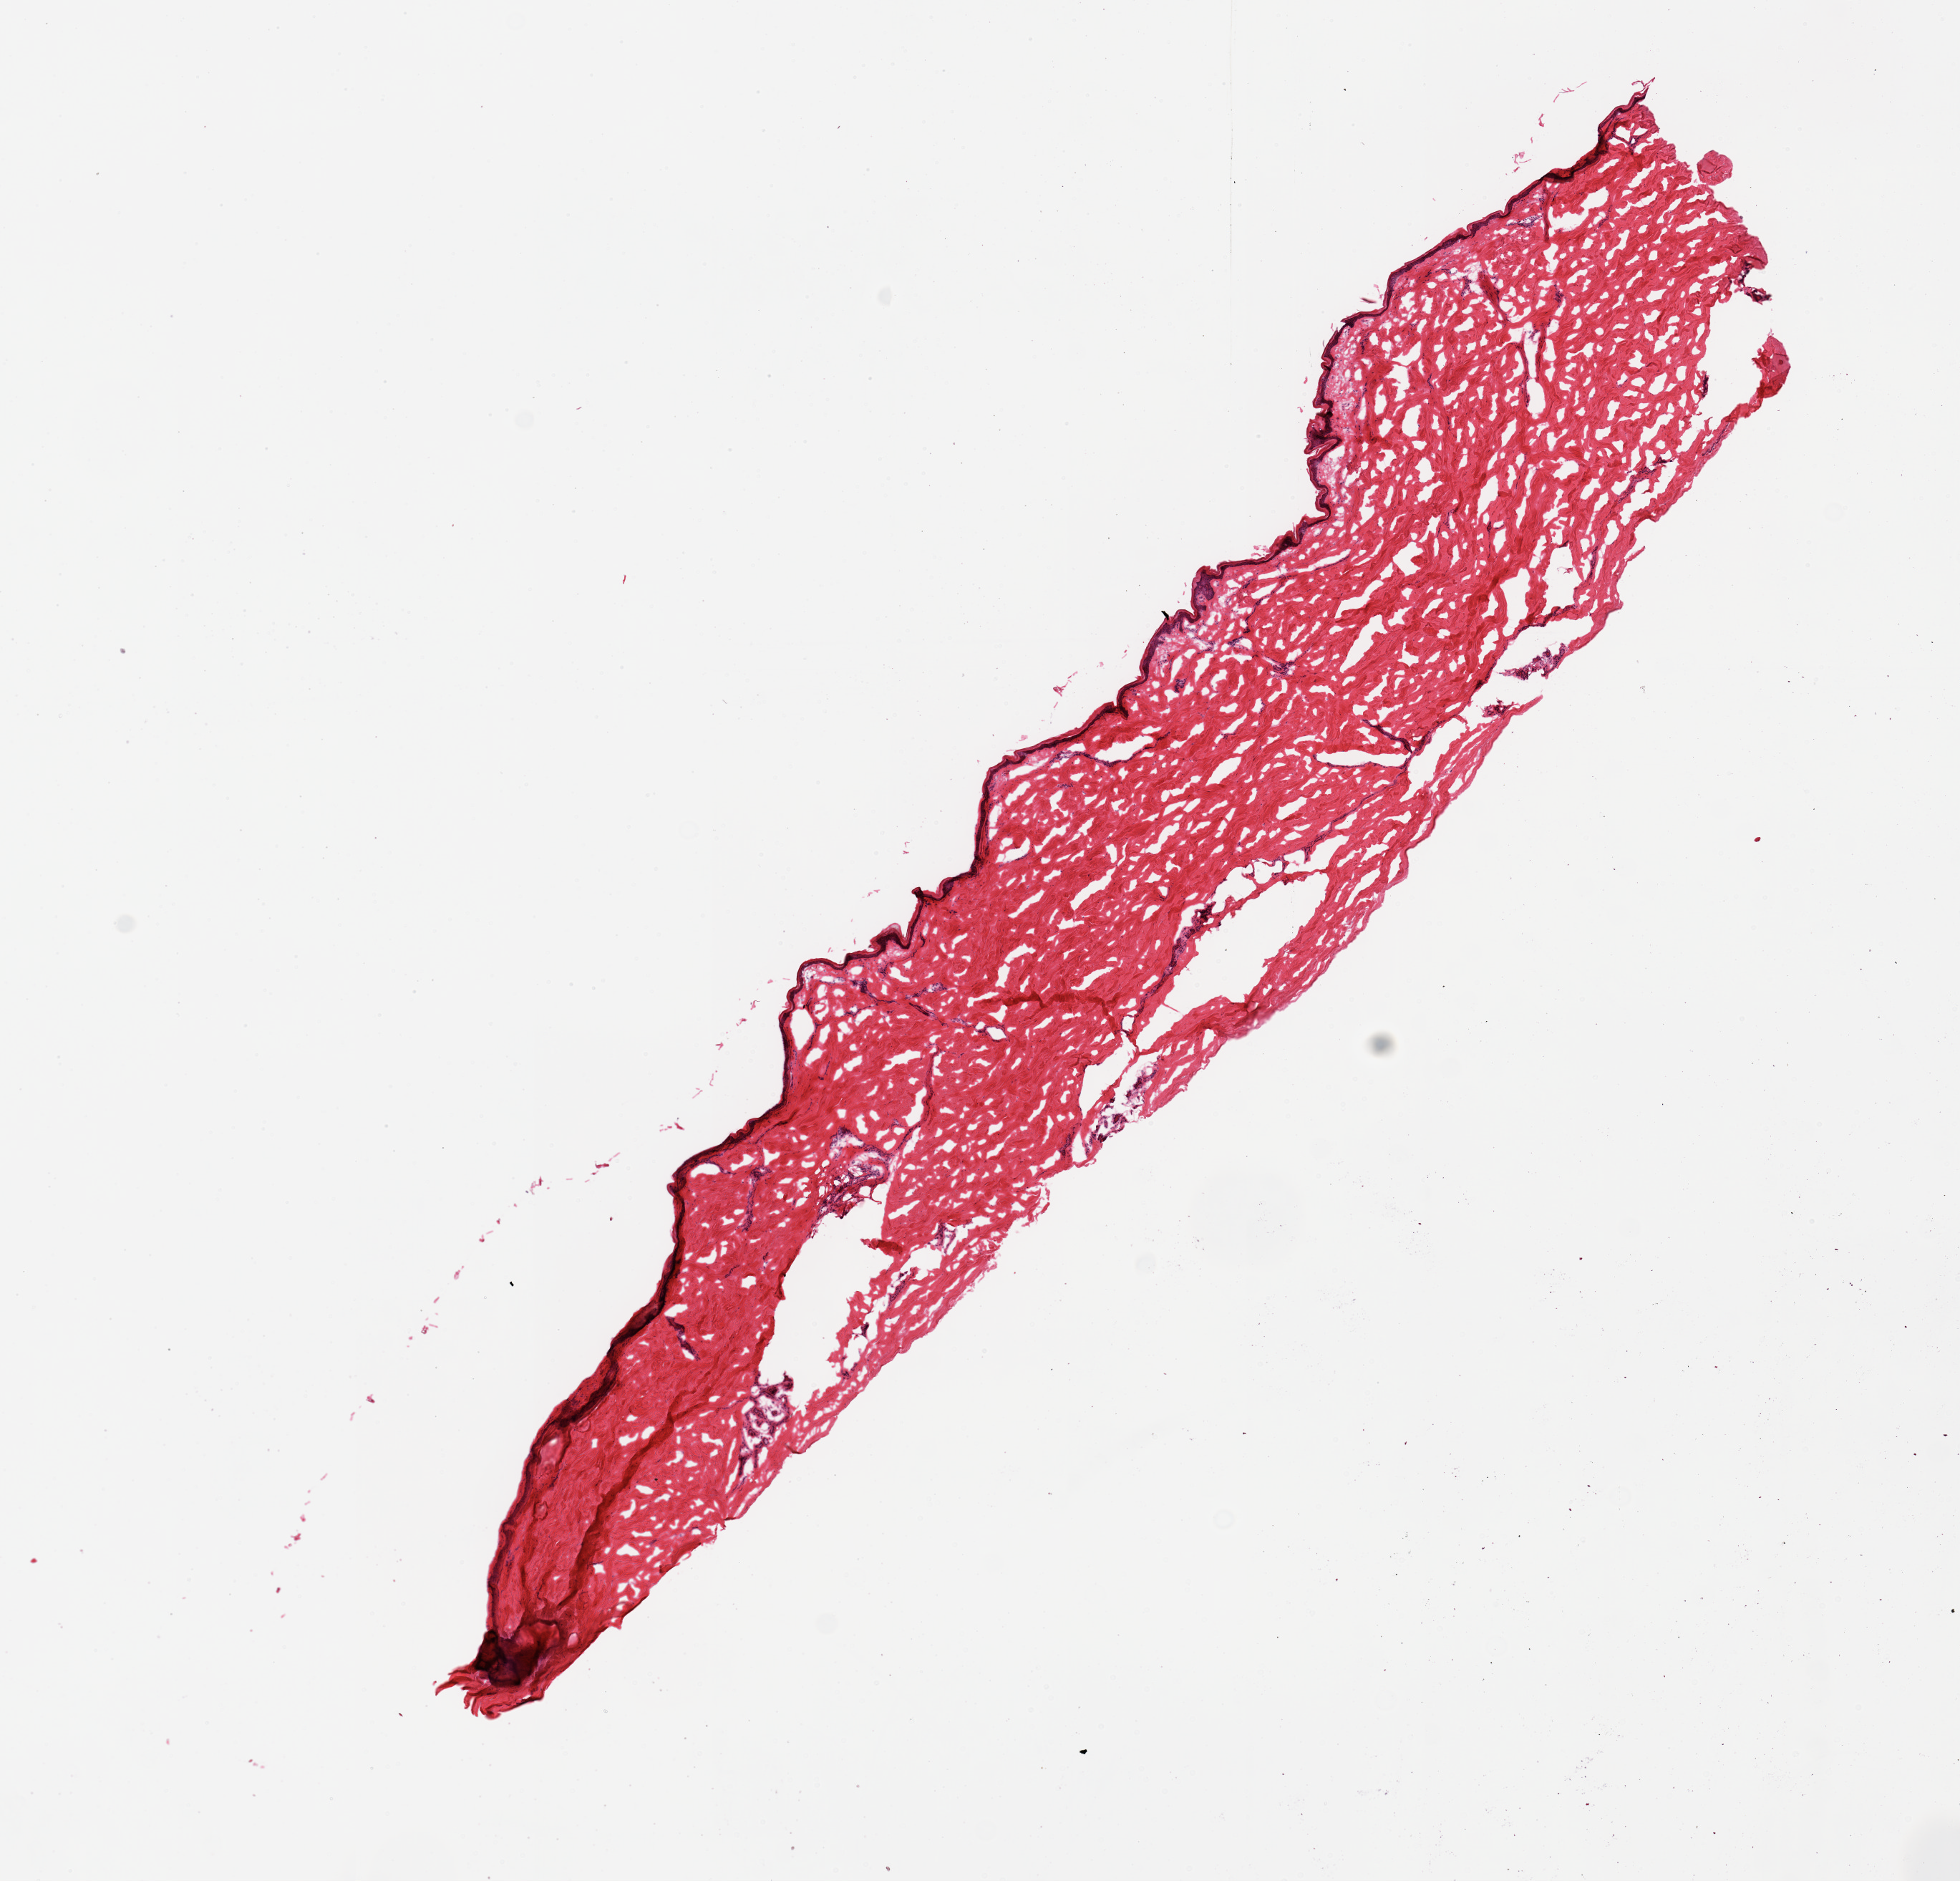
Haematoxylin and eosin whole-slide image, shown as a low-resolution overview of the whole scanned area (about 10.8 x 10.4 mm); frozen section; section of skin of lower leg (target tissue); donor tissue sample. Donor sex: male.
- pathologist's review note for this sample: 1 piece; well trimmed